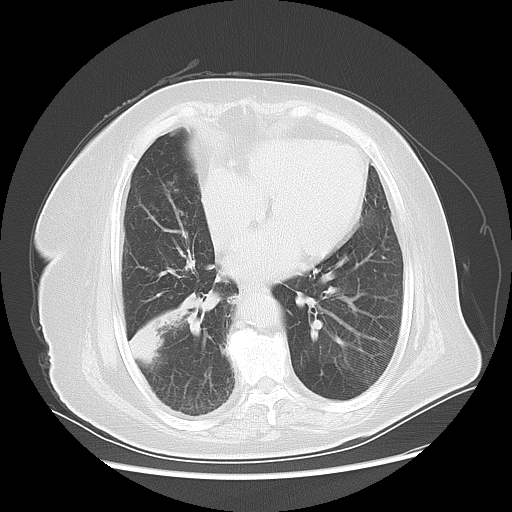
Chest CT, one axial slice; position 23 of 56 along the scan axis; 120 kVp; lung window (W 1500 / L -600 HU); 512 × 512 image matrix. Patient: female, 73 years. Case-level facts recorded for this patient, not image findings: clinical TNM (as recorded): T3 N0 M0.
Outlined on this slice (bounding box drawn by a radiologist):
- lung tumour (recorded histology: adenocarcinoma): box from (x=124, y=303) to (x=188, y=369) px